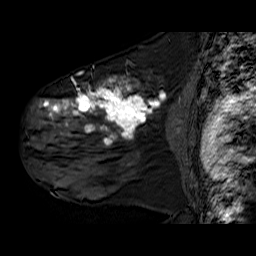
Breast MRI (dynamic contrast-enhanced), one sagittal slice; position 39 of 60 along the scan axis; dynamic contrast-enhanced series, time point 2 of 6 at this slice position (early post-contrast); 1.5 T; TE 6.3 ms, TR 32.9 ms; 4 mm slice thickness; 256 × 256 image matrix. Female patient. Case-level facts recorded for this patient, not image findings: setting: breast cancer imaged before/during neoadjuvant chemotherapy; receptor status: HER2-positive.
Annotated regions visible in this slice (semi-automatically segmented with operator editing):
- analysis volume of interest (the breast-tissue region the enhancement analysis was run in; not a lesion): bounding box <30,78,176,180> (left, top, right, bottom; pixels)
- tumour enhancement mask (voxels above the 100 % enhancement threshold inside the analysis volume of interest): <43,78,165,144>